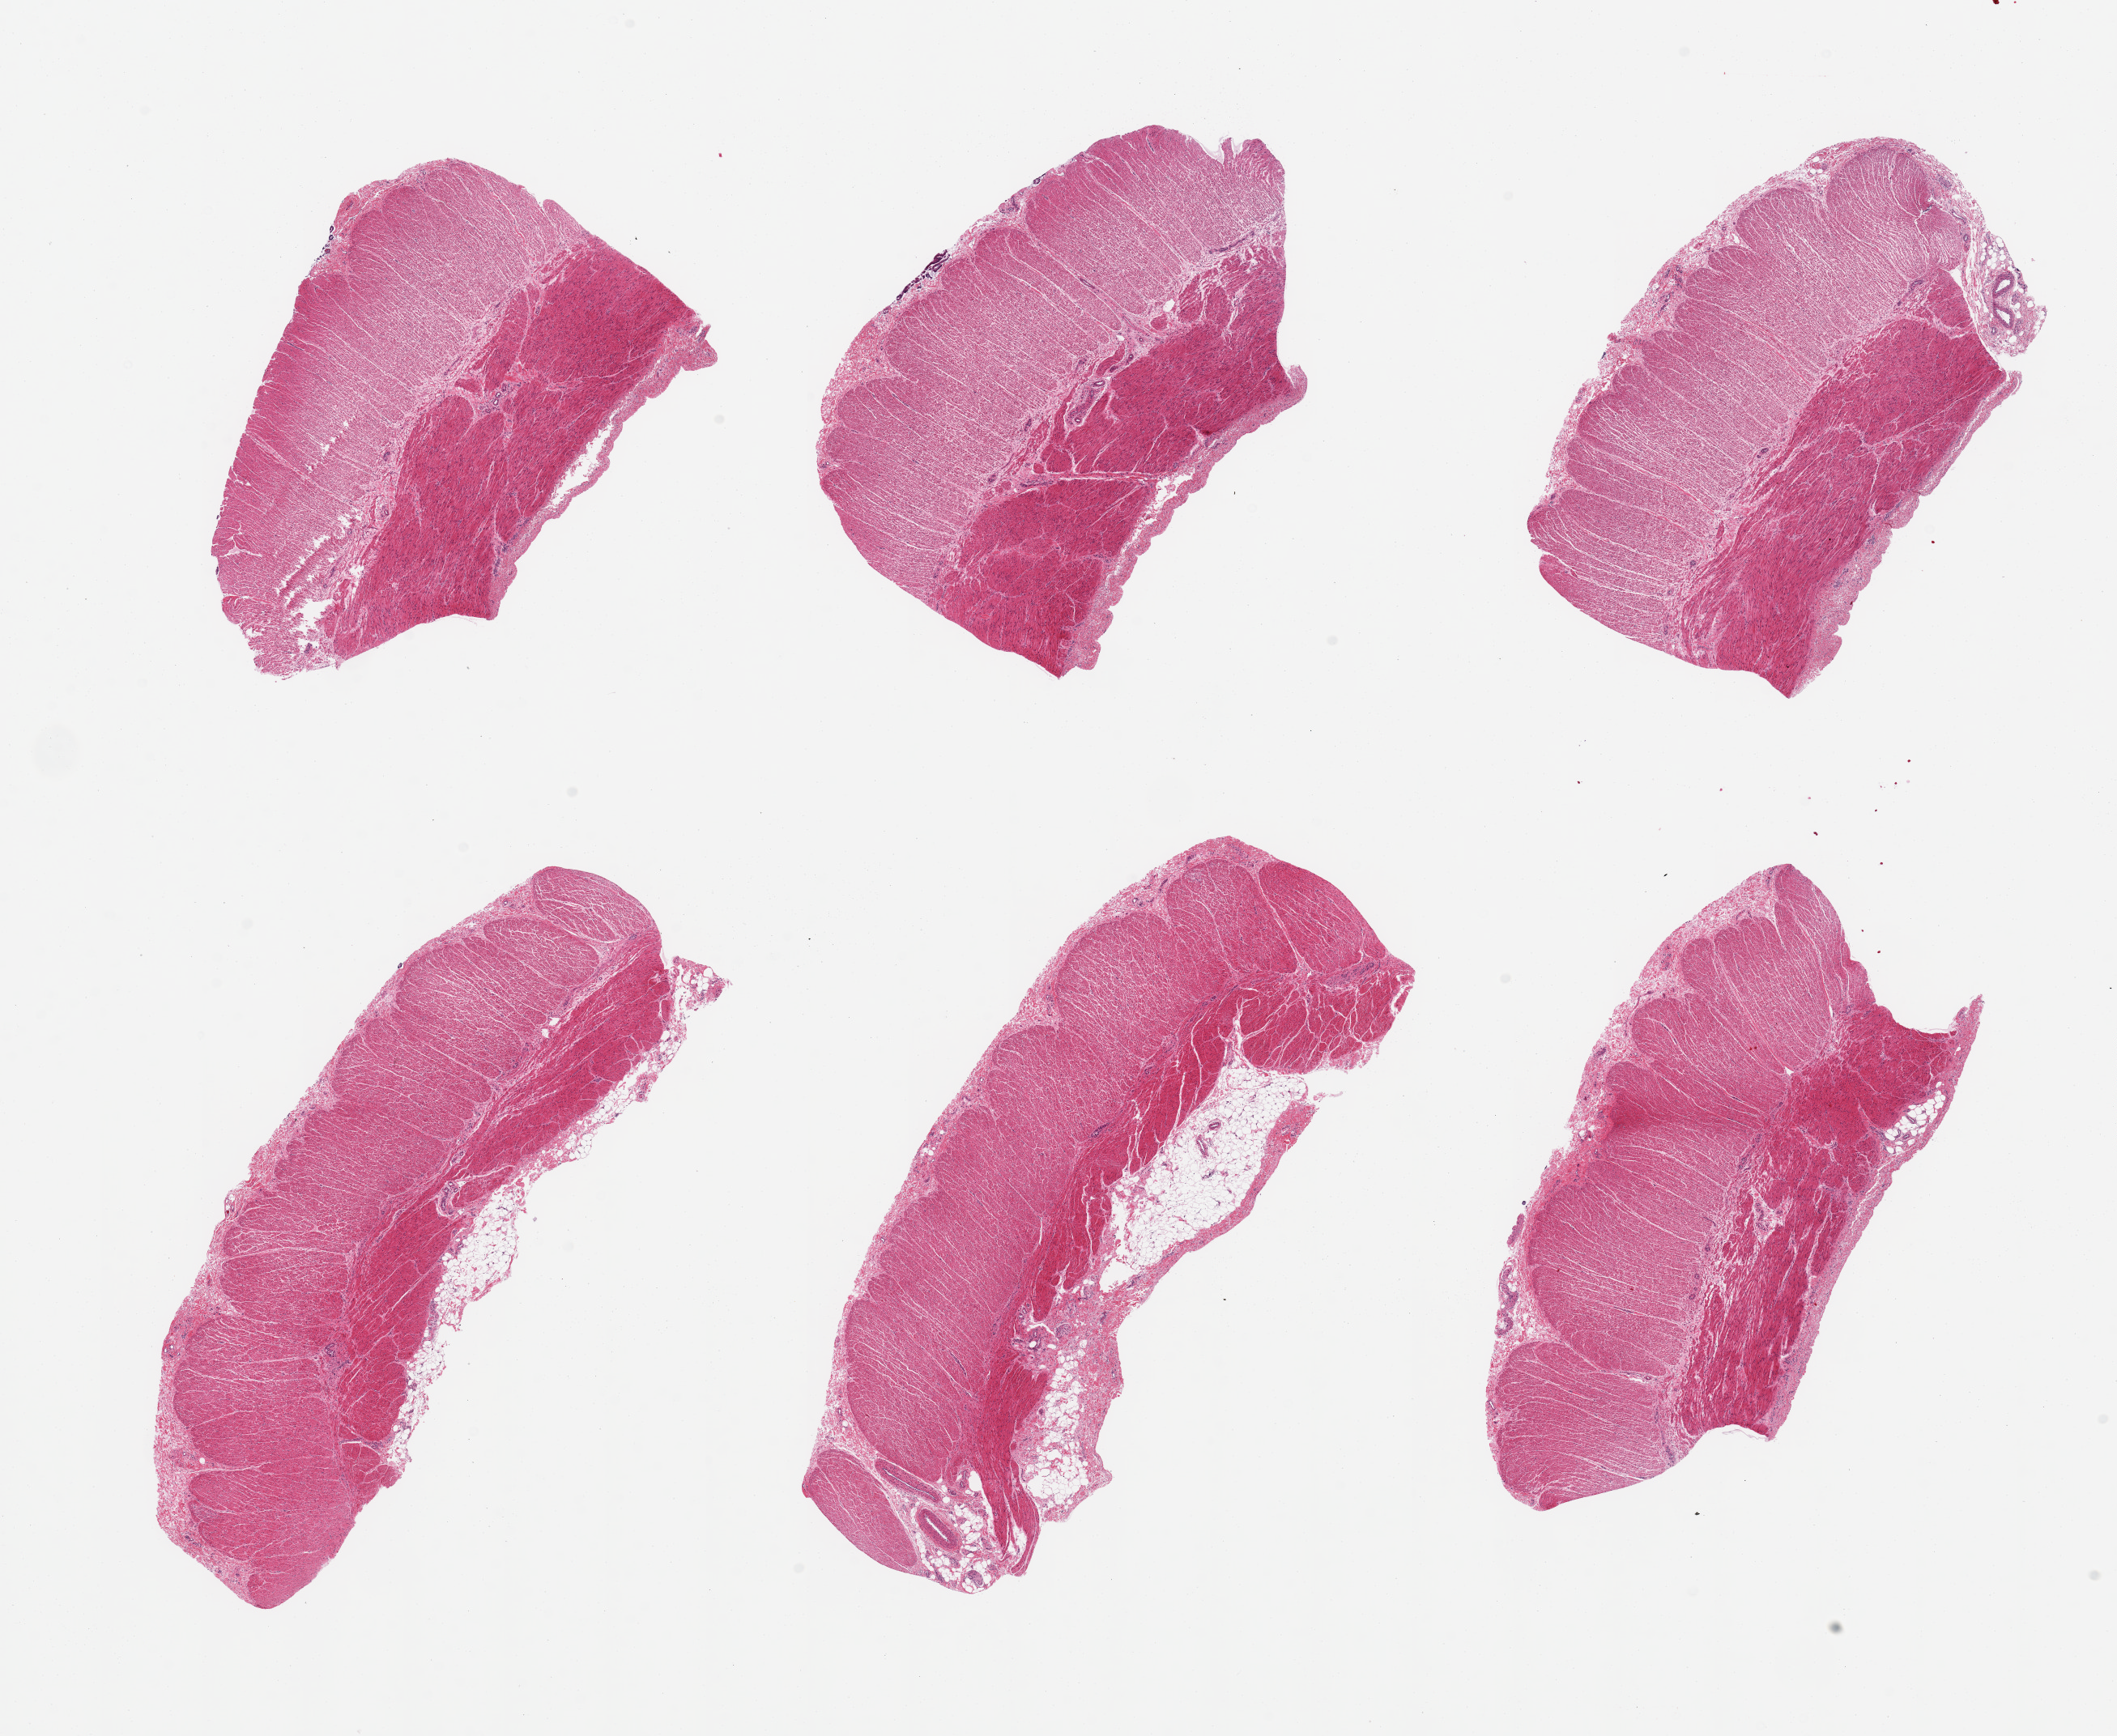
Hematoxylin and eosin (H&E) whole-slide image, whole scanned area (about 20.7 x 17.0 mm, slide scanned at 20x) shown as a low-resolution overview; PAXgene-fixed, paraffin-embedded tissue; target tissue: sigmoid colon; donor tissue sample. Donor: female.
Reviewer comment on this tissue sample: 6 pieces; generally well dissected; 1 has 1mm fibrofatty adventitia.